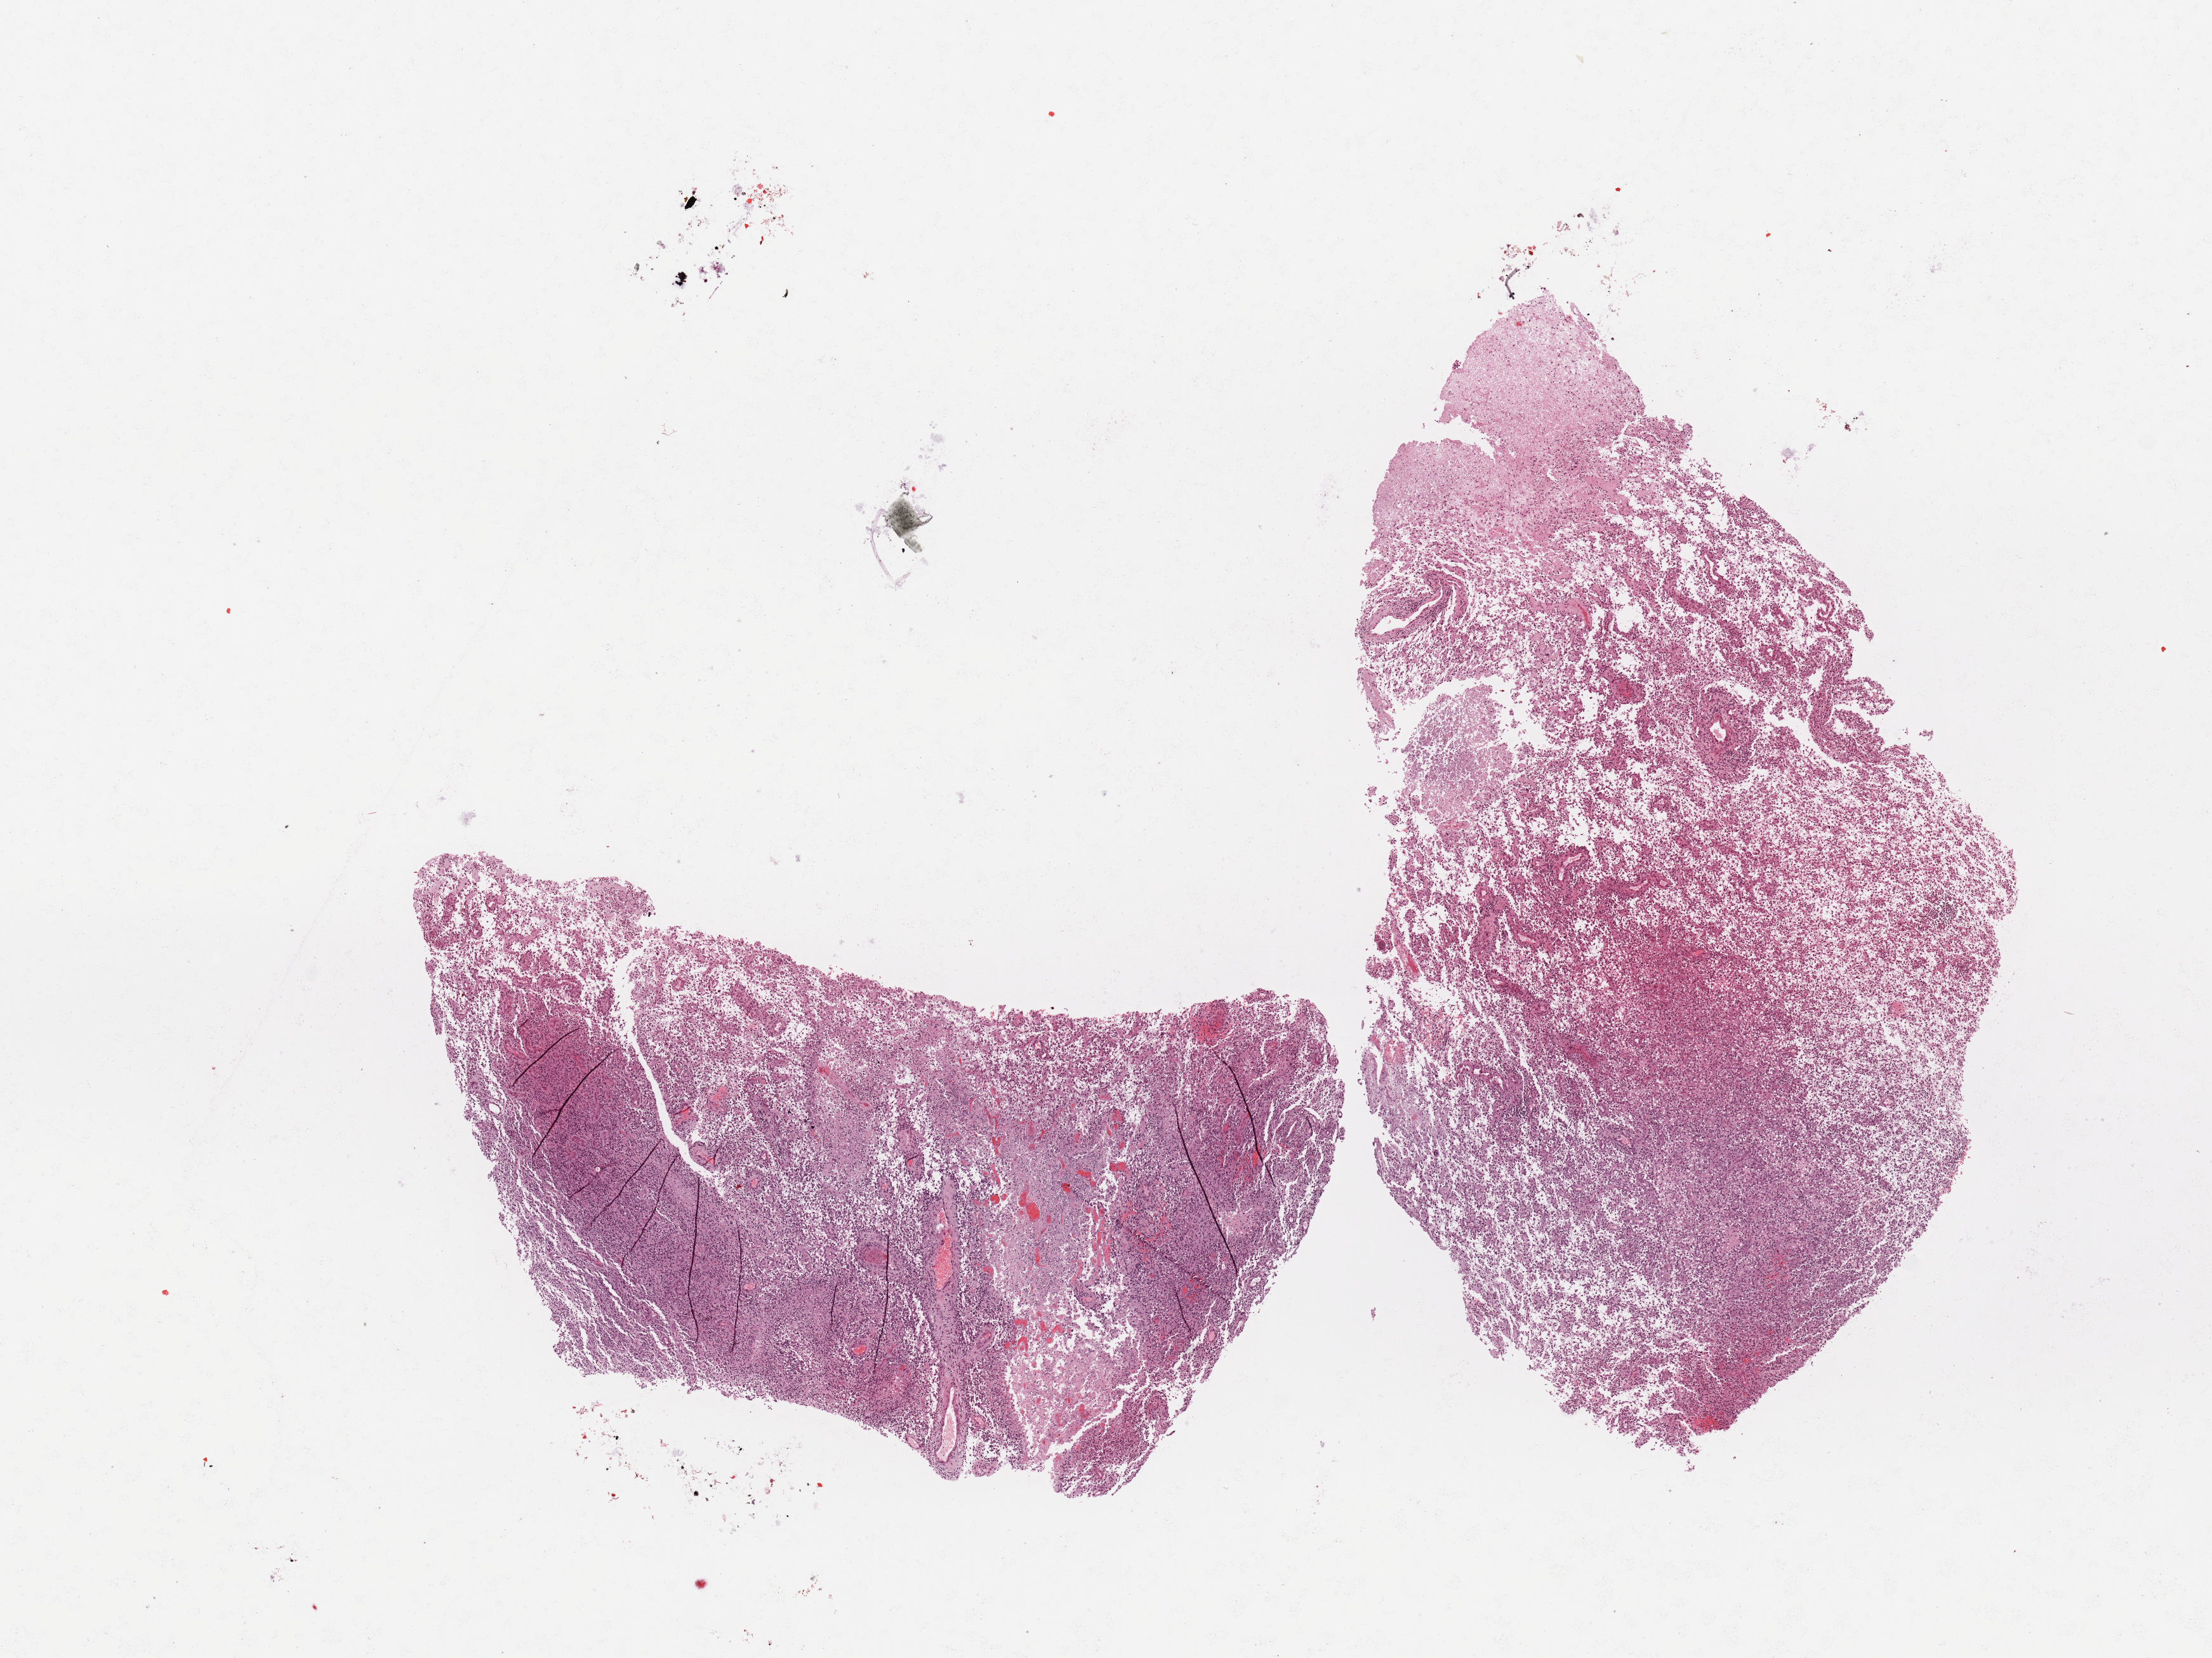
Digitized H&E tissue section (whole slide), low-resolution overview of the scanned area, about 13.8 x 10.3 mm (acquisition: 20x scan). Tumour tissue sample, sampled site: frontal lobe. 44-year-old male patient. Composition of this section per pathologist review: tumour nuclei 80%, necrosis 30%.
- histologic diagnosis: Glioblastoma
- primary tumour site (as recorded): frontal lobe